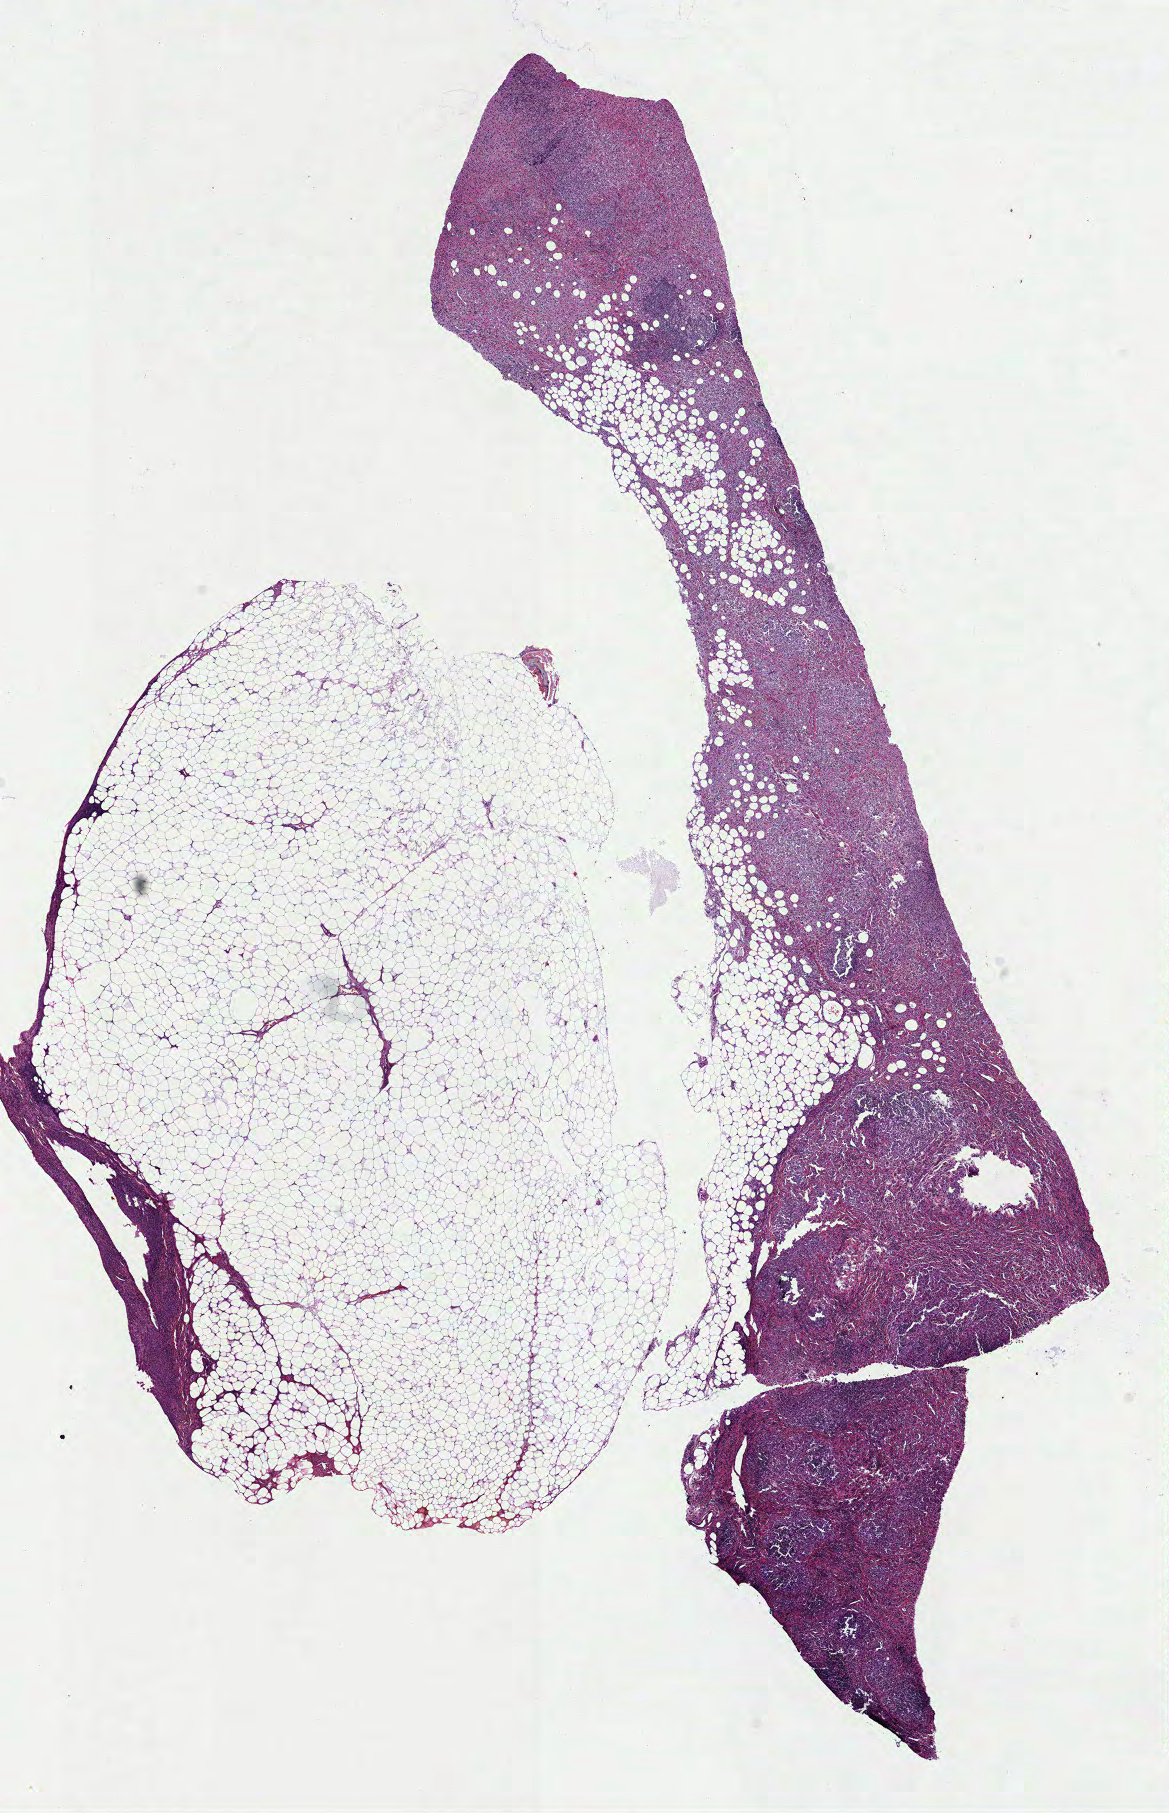
Whole-slide histology image, Hematoxylin and eosin (H&E) stained, whole scanned area (about 9.4 x 14.6 mm) shown as a low-resolution overview. Formalin-fixed paraffin-embedded (FFPE) diagnostic section. Primary tumour sample from the breast. Female patient; age at initial diagnosis 49 years.
Histologic diagnosis: Lobular carcinoma, NOS. AJCC pathologic stage: IIIC. Lymph nodes positive (case pathology): 19 of 21 examined. Laterality: left.